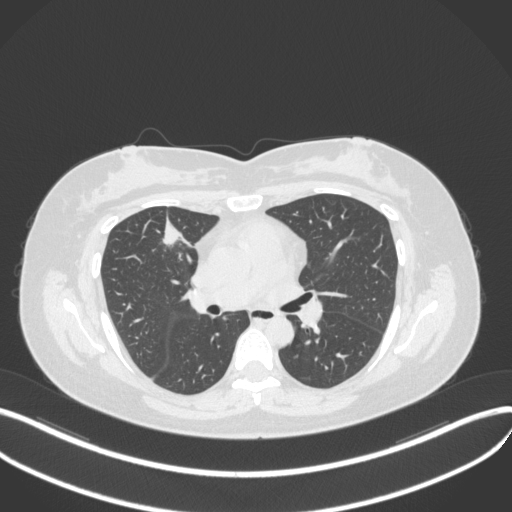
Chest CT, one axial slice; position 180 of 272 along the scan axis; 120 kVp; lung window (W 1500 / L -600 HU); 1 mm slice thickness; 512 × 512 image matrix, field of view 400 × 400 mm. Female patient, age 42 years. Case-level facts recorded for this patient, not image findings: clinical TNM (as recorded): T1b N0 M0.
Structures marked on this image (rectangle marked by the reading radiologist):
- lung tumour (recorded histology: adenocarcinoma): box from (x=157, y=214) to (x=186, y=248) px